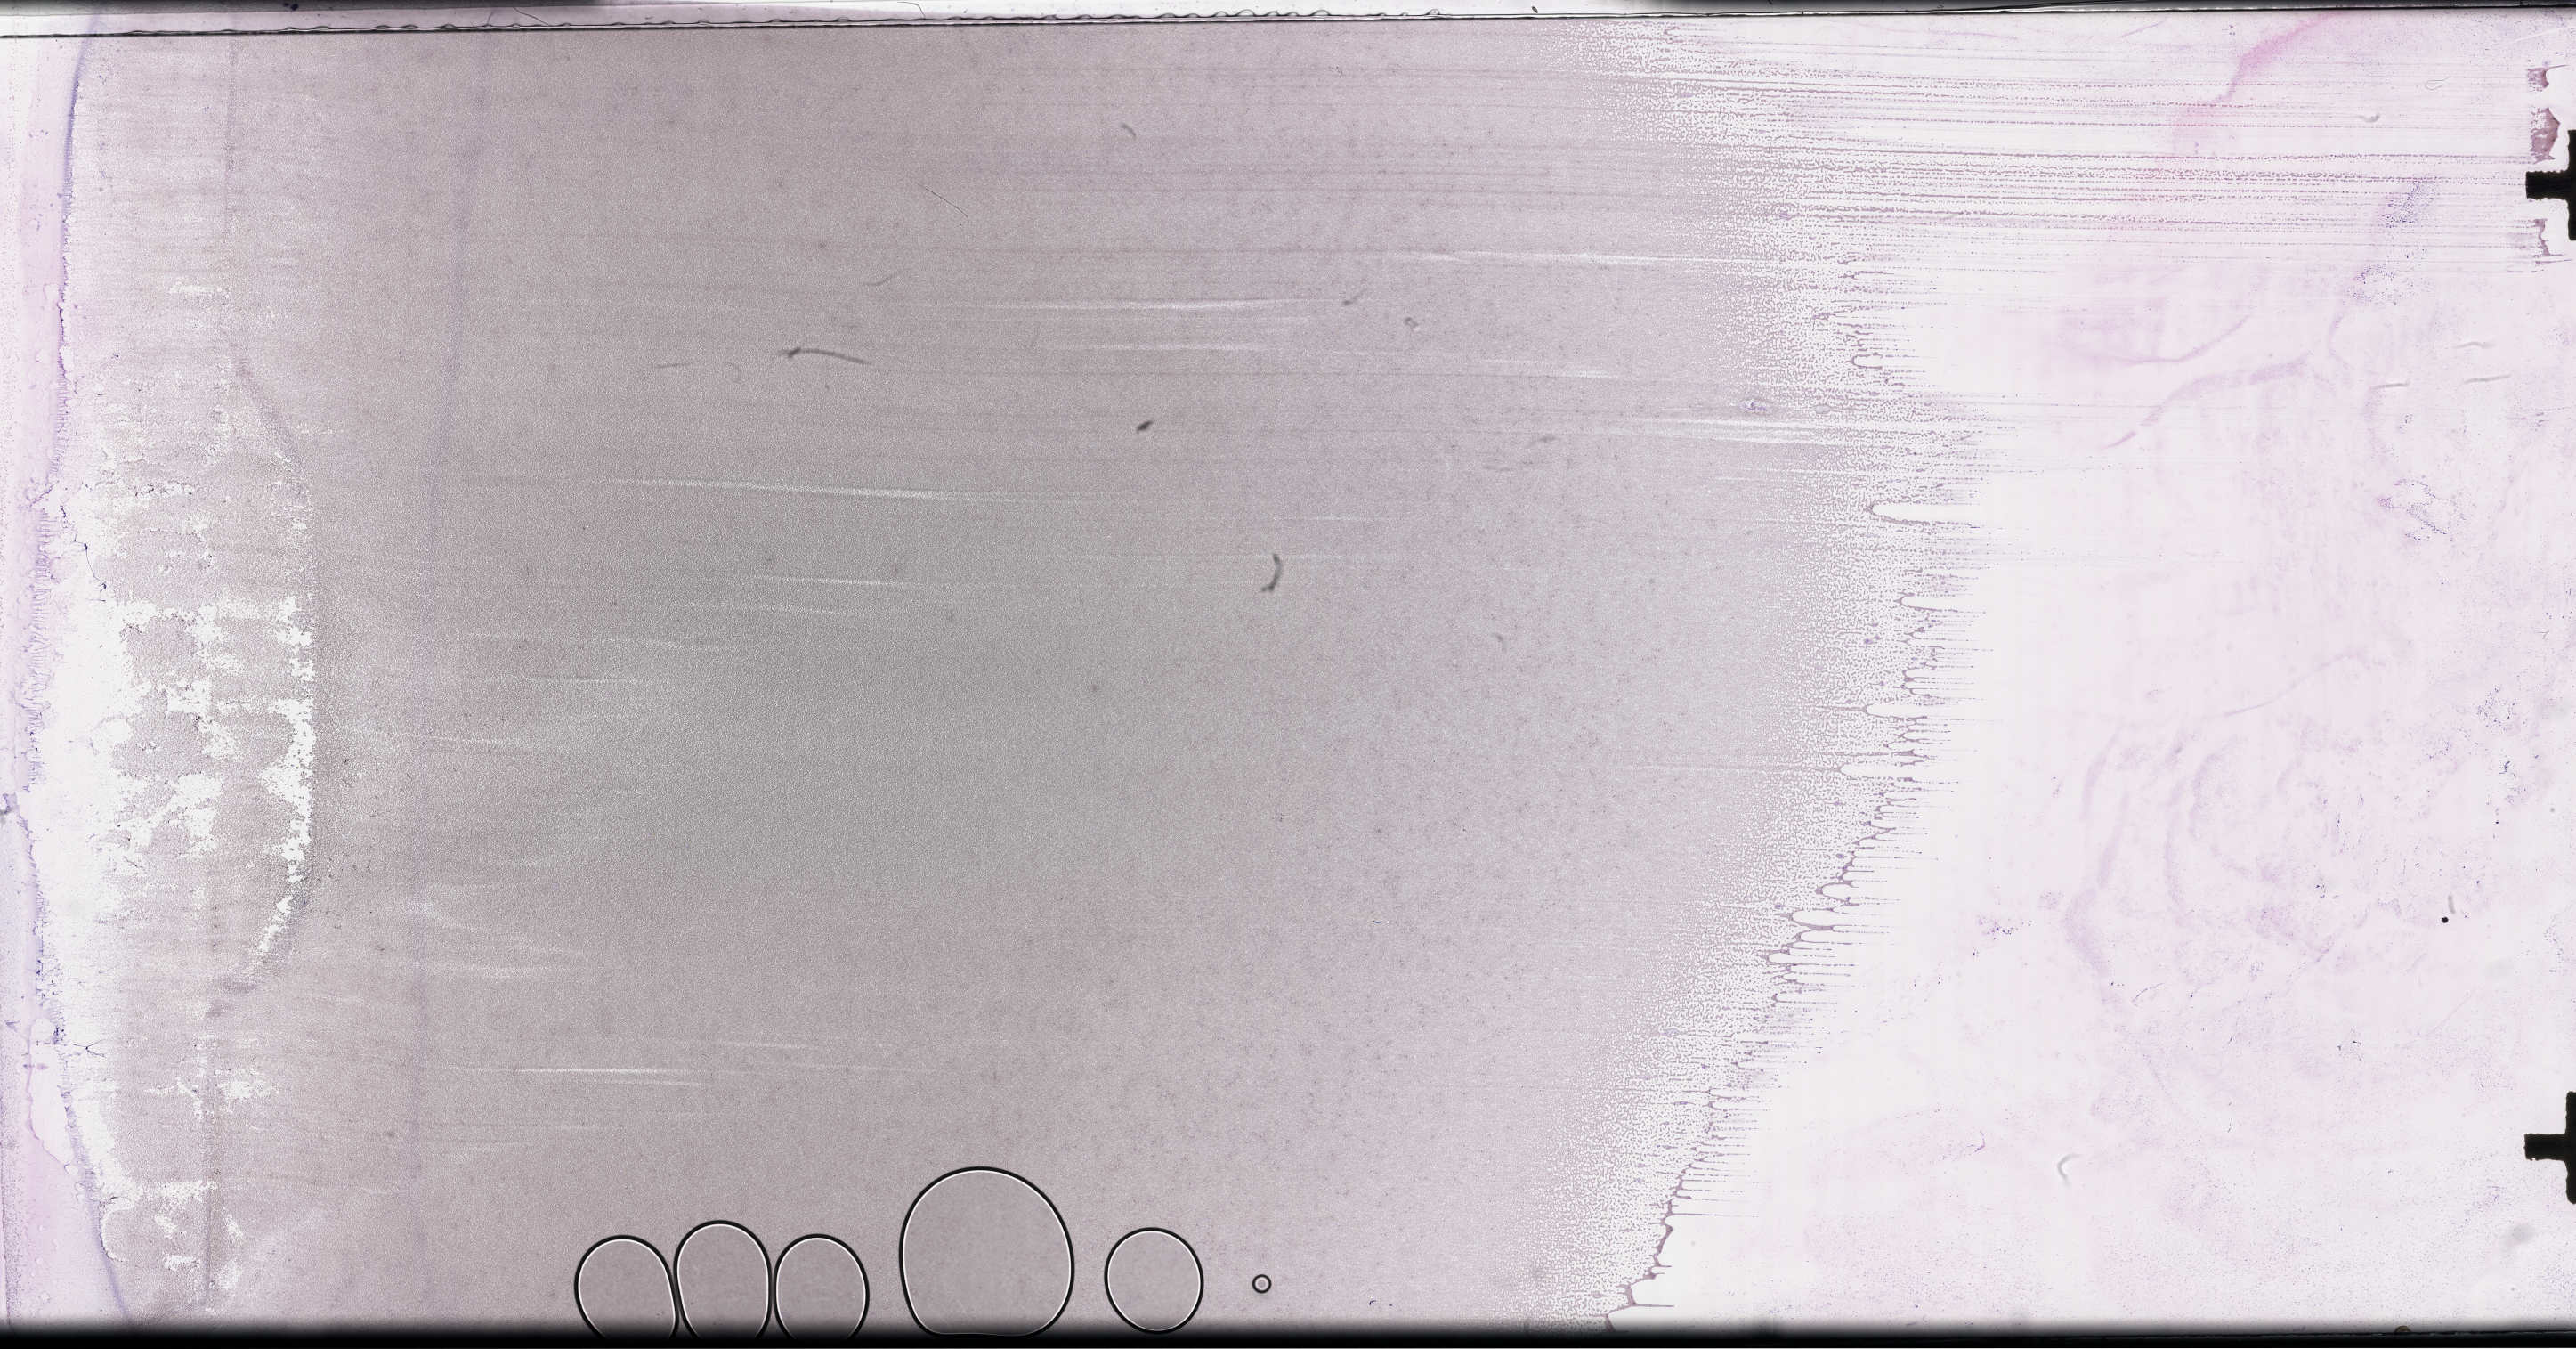
Wright–Giemsa-stained whole blood smear, whole-slide image, whole scanned area (about 46.7 x 24.5 mm) shown as a low-resolution overview. EDTA-anticoagulated smear. Collected on treatment. Patient sex: female.
- from a patient with: Plasma Cell Myeloma